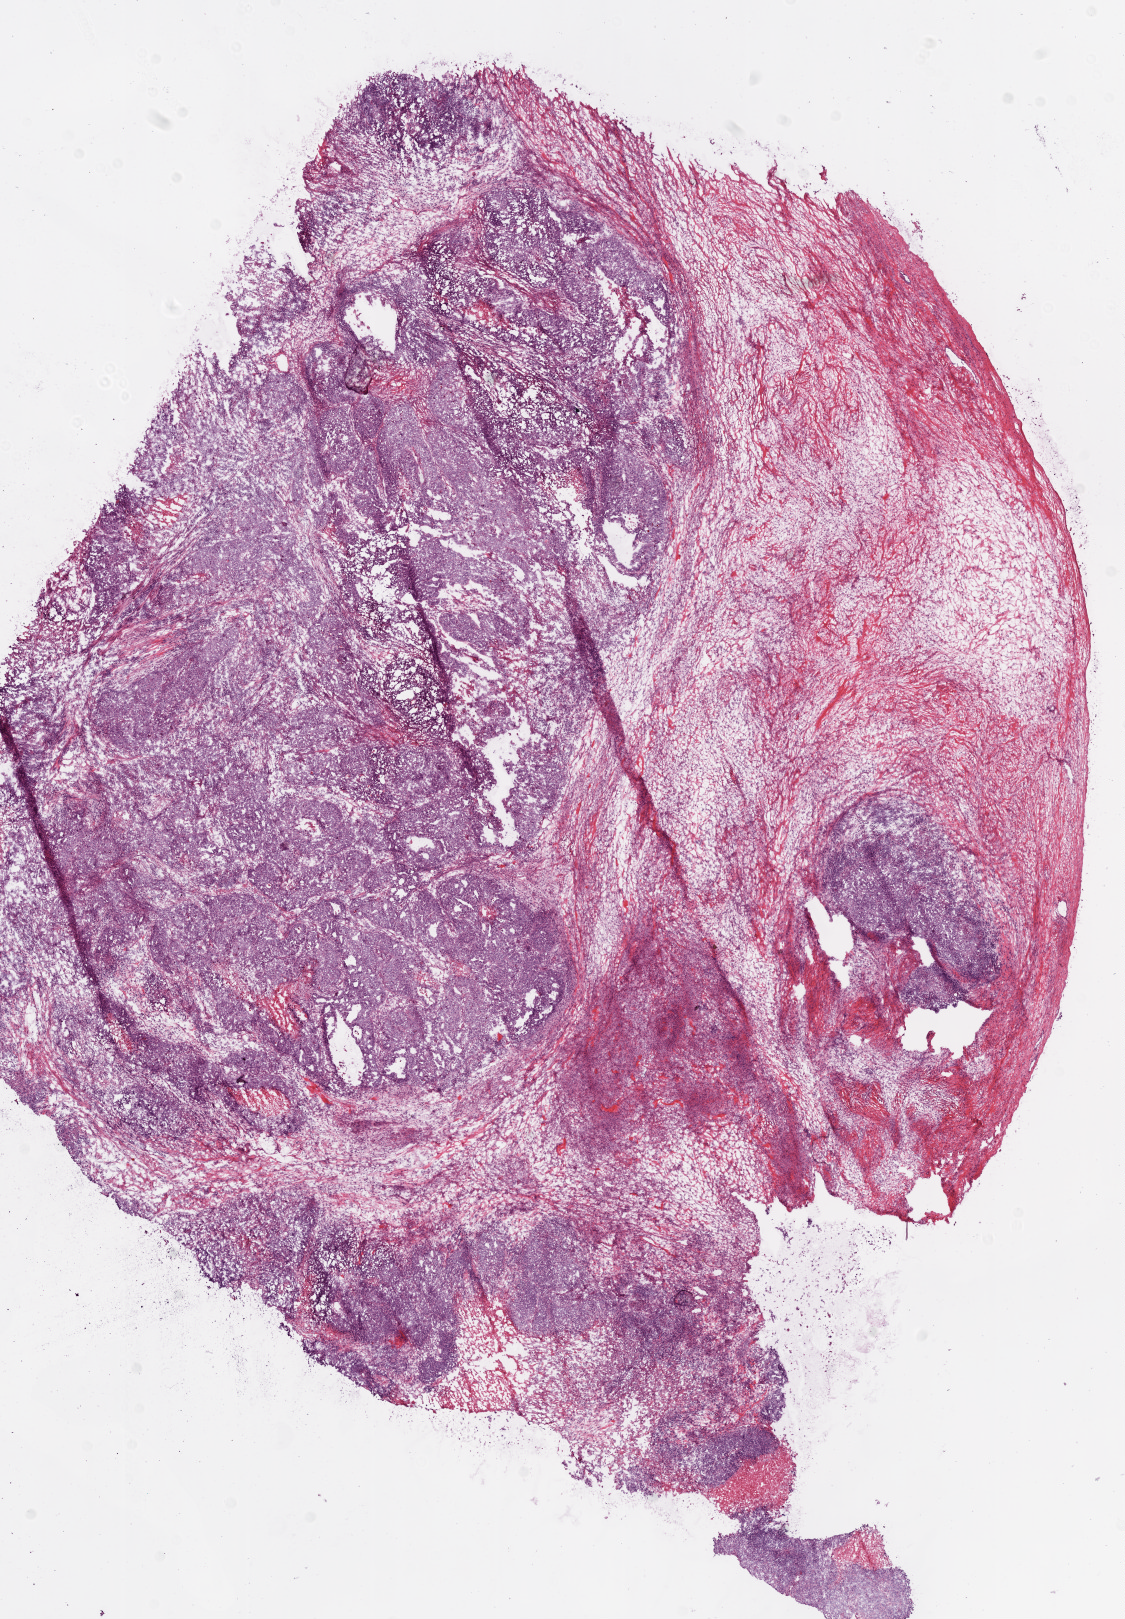
Whole-slide histology image, H&E-stained — a low-resolution overview of the entire scanned area, about 9.0 x 13.0 mm, frozen section from the bottom of the tissue portion, primary tumour sample from the ovary. Patient sex: female. Histologic grade: G3 (poorly differentiated). Pathologist review of this section (percent, as recorded): tumour cells 65%, tumour nuclei 95%, normal cells 0%, stromal cells 25%, necrosis 10%.
FIGO stage: IB. Laterality: bilateral. Pathologic diagnosis: Serous cystadenocarcinoma, NOS.